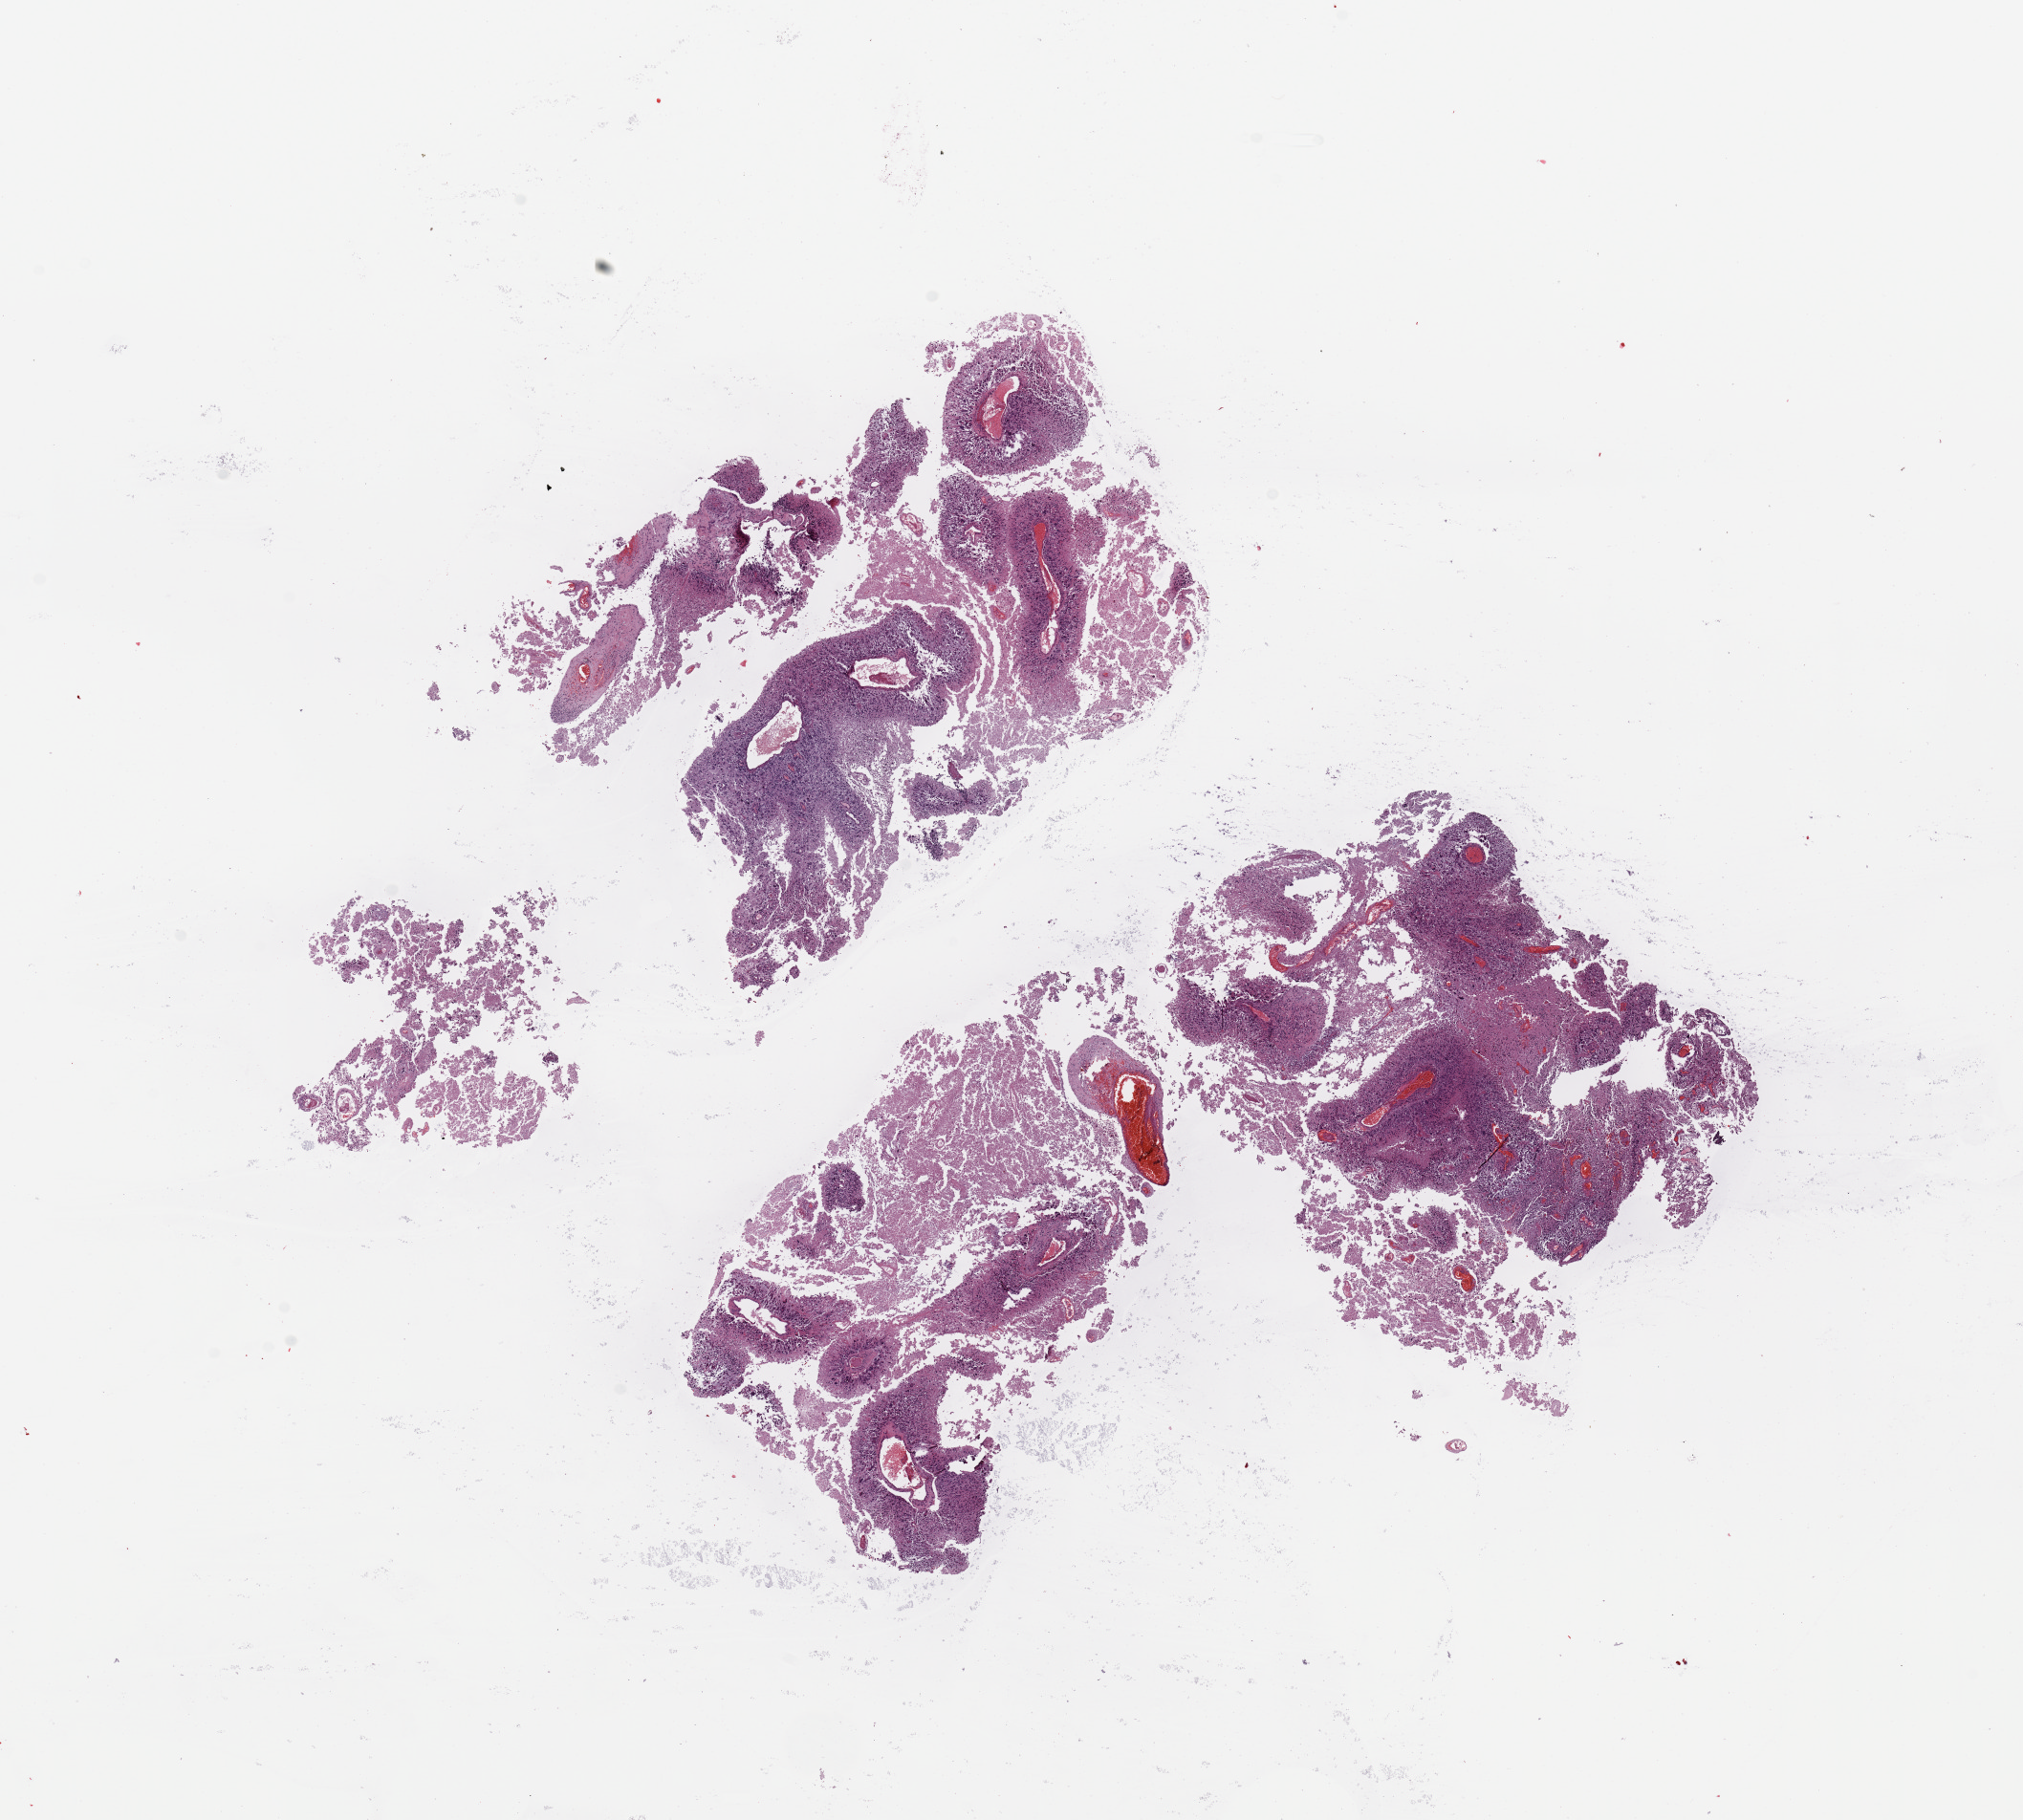
H&E whole-slide image, a low-resolution overview of the entire scanned area, about 16.7 x 15.1 mm (from a 20x scan). Tumour tissue sample, brain. Patient: female, age 61 years.
- histologic diagnosis: Glioblastoma
- primary tumour site (as recorded): frontal lobe